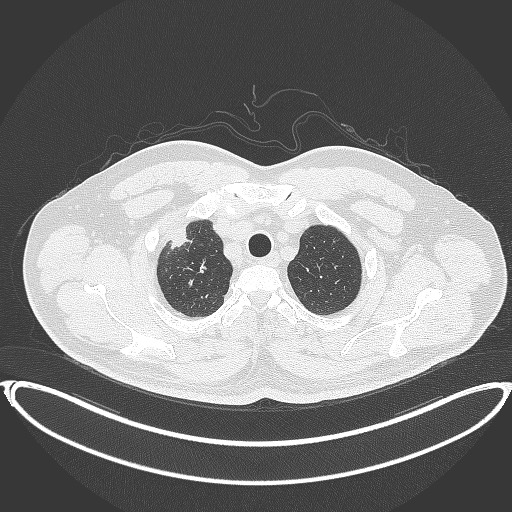
Chest CT, one axial slice. Slice 342 of 399 in the series (ordered by position). Reconstruction kernel B70f. 120 kVp. Lung window (W 1500 / L -600 HU). 1 mm slice thickness. 512 × 512 image matrix, field of view 445 × 445 mm. Male patient, age 53 years. From the clinical record (not read from this slice): clinical TNM (as recorded): T2a N0 M0.
Outlined on this slice (rectangle marked by the reading radiologist):
- lung tumour (recorded histology: adenocarcinoma): bounding box <164,214,197,256> (left, top, right, bottom; pixels)